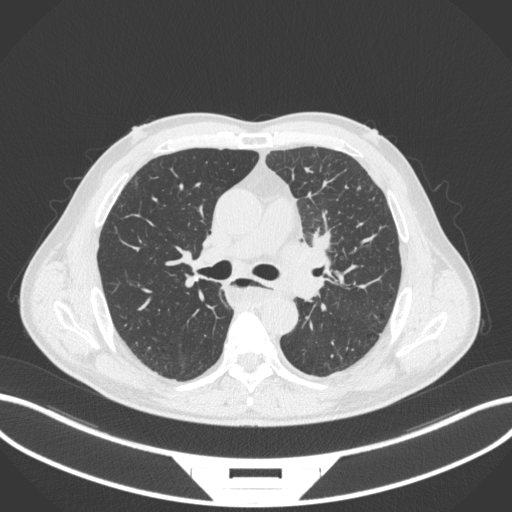
Chest CT, one axial slice; position 232 of 411 along the scan axis; 120 kVp; lung window (W 1500 / L -600 HU); 1 mm slice thickness; 512 × 512 image matrix, field of view 400 × 400 mm. Patient: male, 57 years. Case-level facts recorded for this patient, not image findings: clinical TNM (as recorded): T2a N1 M0.
Outlined on this slice (rectangle marked by the reading radiologist):
- lung tumour (recorded histology: squamous cell carcinoma): box from (x=279, y=227) to (x=347, y=275) px